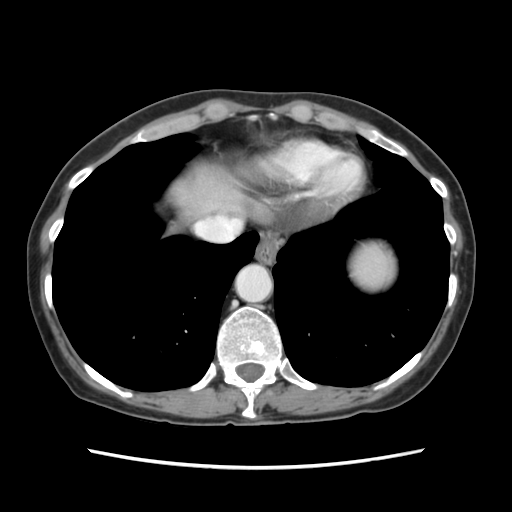
Contrast-enhanced abdominal CT, one axial slice; slice 108 of 120 in the series (ordered by position); intravenous contrast given; soft-tissue window (W 400 / L 40 HU); 2.5 mm slice thickness; 512 × 512 image matrix, field of view 330 × 330 mm. Female patient, age 70 years. Case-level facts recorded for this patient, not image findings: diagnosis: colorectal cancer liver metastases, imaged before liver resection; multiple liver metastases: no; largest metastasis: 2.5 cm; disease in both lobes: no.
Annotated regions visible in this slice (expert manual segmentation):
- liver: bounding box (x1, y1, x2, y2) in pixels: (170, 167, 245, 217)
- planned liver remnant (the part of the liver to remain after resection): (172, 168, 244, 217)